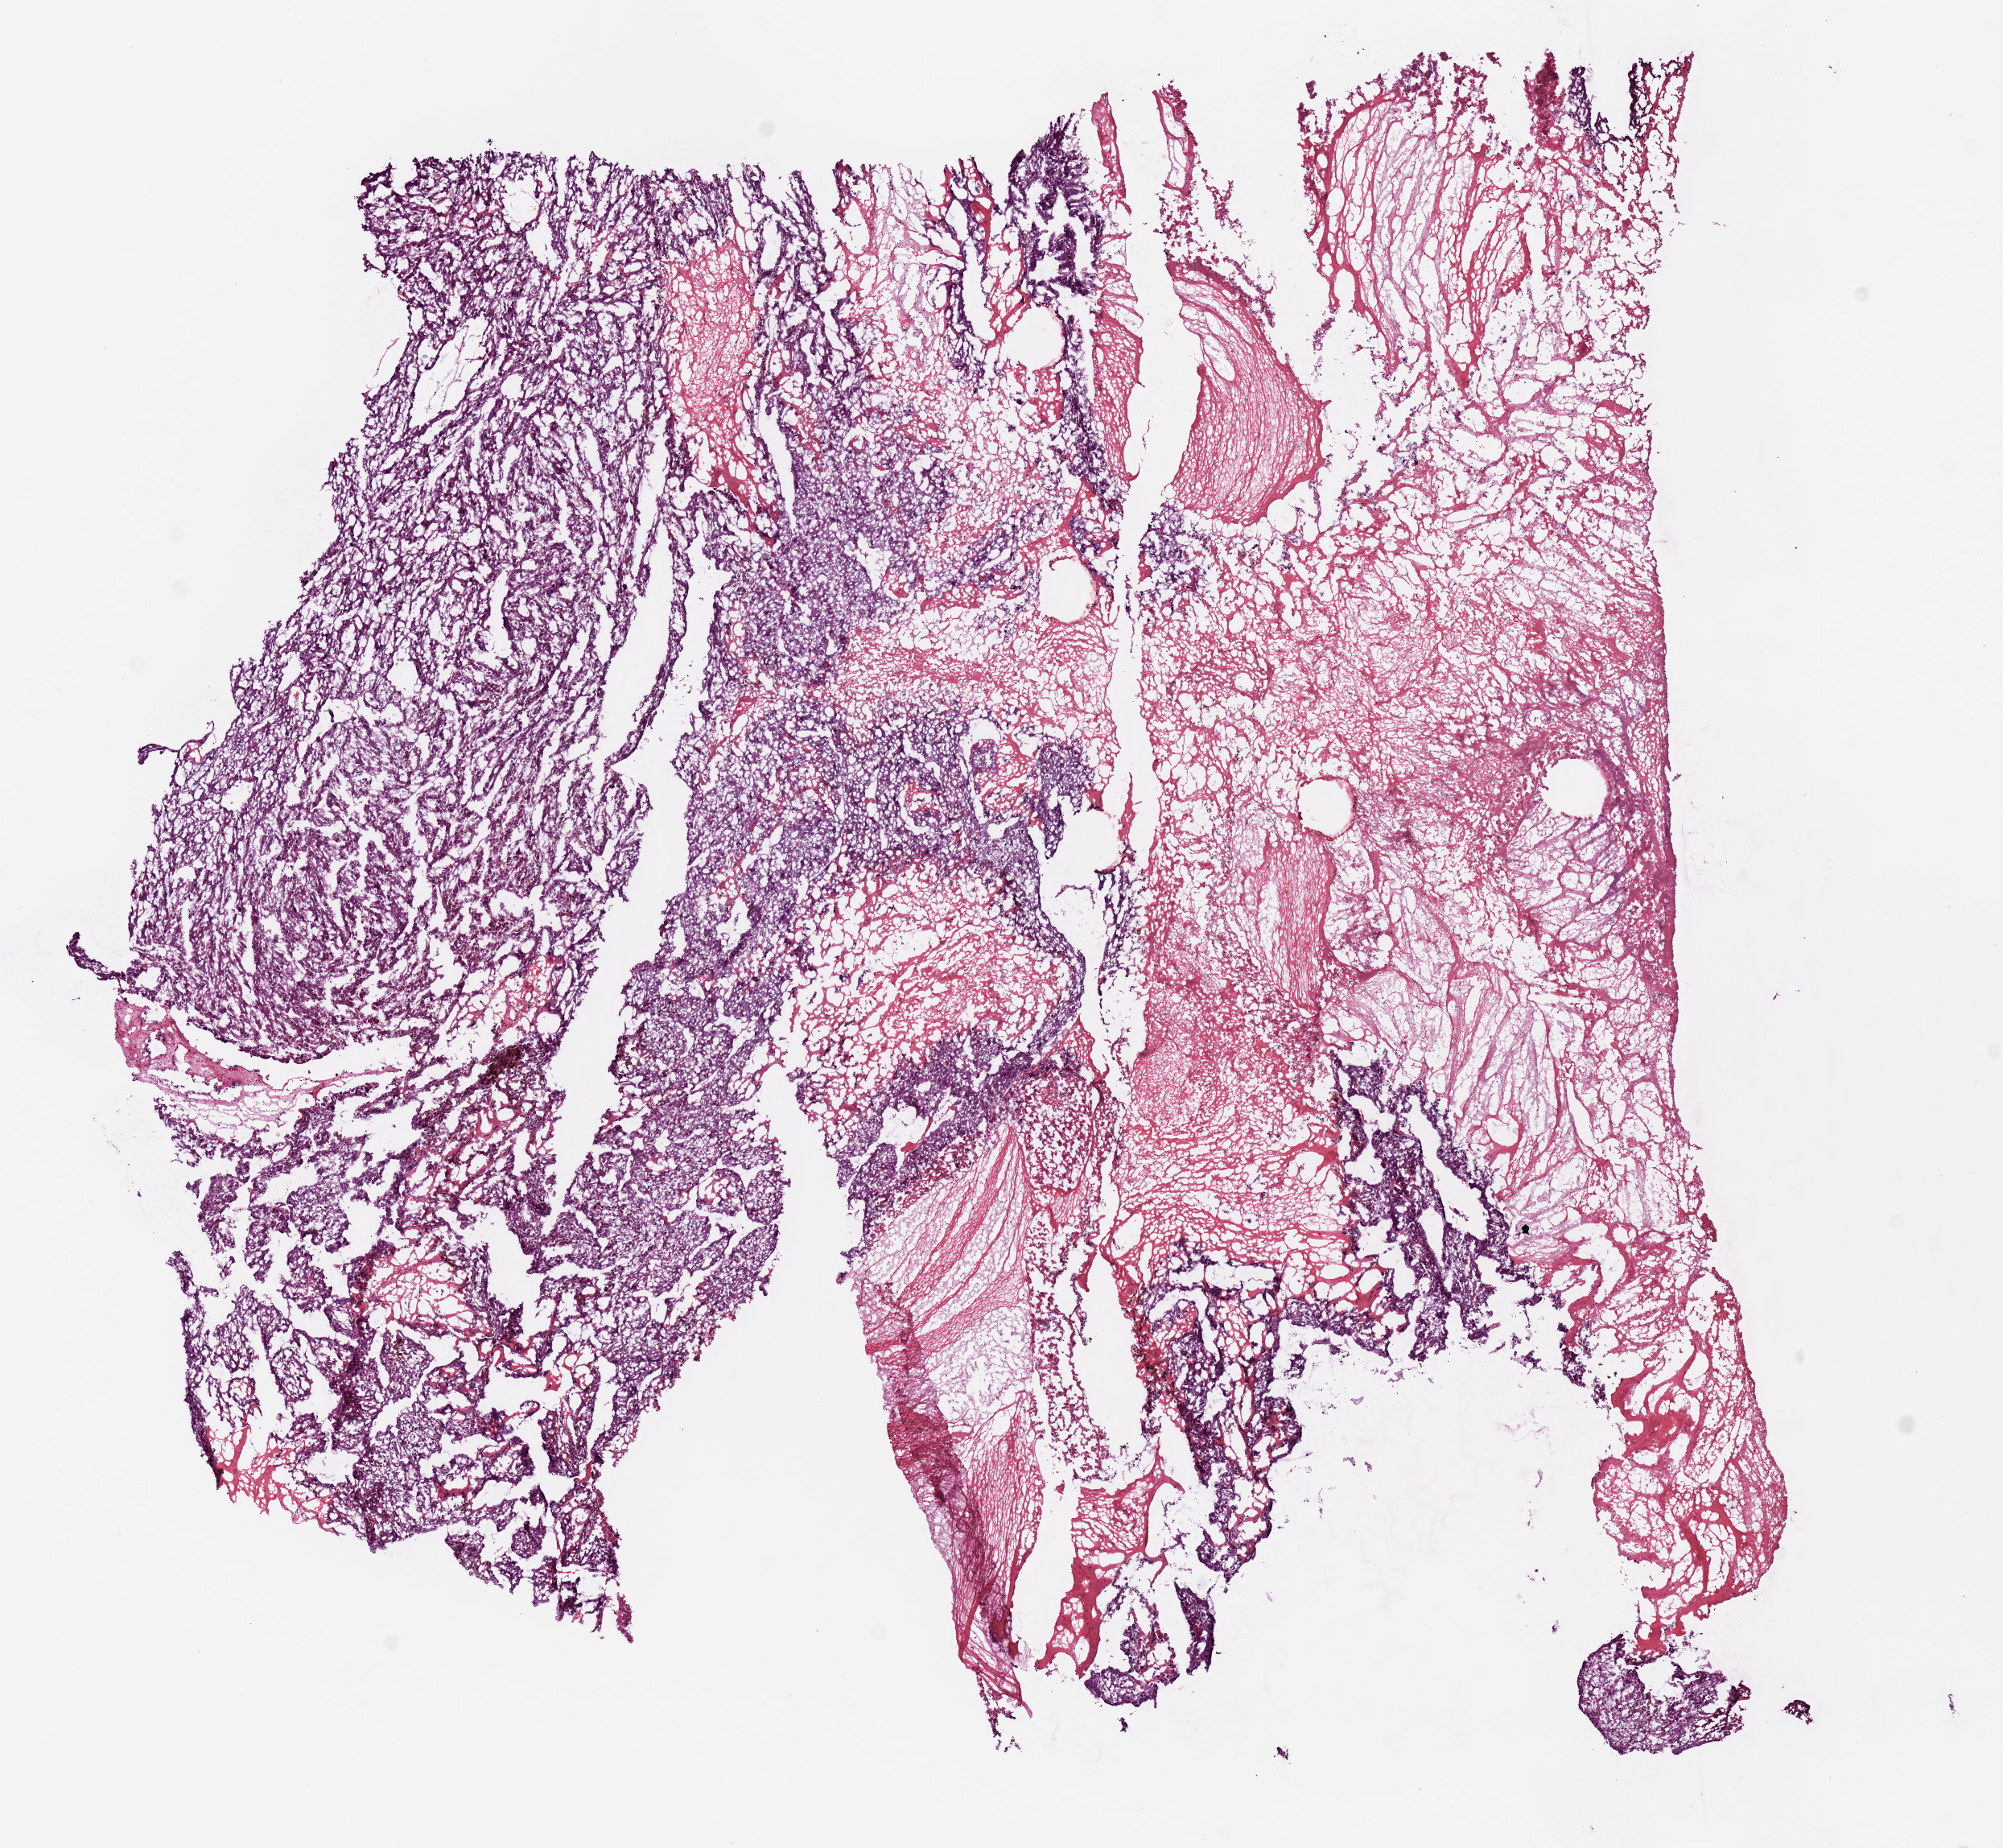
Digitized Hematoxylin and eosin (H&E) stained tissue section (whole slide) — whole scanned area (about 9.8 x 9.1 mm) shown as a low-resolution overview. Frozen section from the top of the tissue portion. Liver, primary tumour sample. Patient: female, age at initial diagnosis 60 years. Histologic grade: G2 (moderately differentiated). Composition of this section per pathologist review: tumour cells 95%, tumour nuclei 75%, normal cells 0%, stromal cells 5%, necrosis 0%. Inflammatory infiltration, as recorded: lymphocyte infiltration 0%, monocyte infiltration 0%, neutrophil infiltration 0%.
Histologic diagnosis: Hepatocellular carcinoma, NOS. AJCC pathologic stage: IIIC (7th edition).